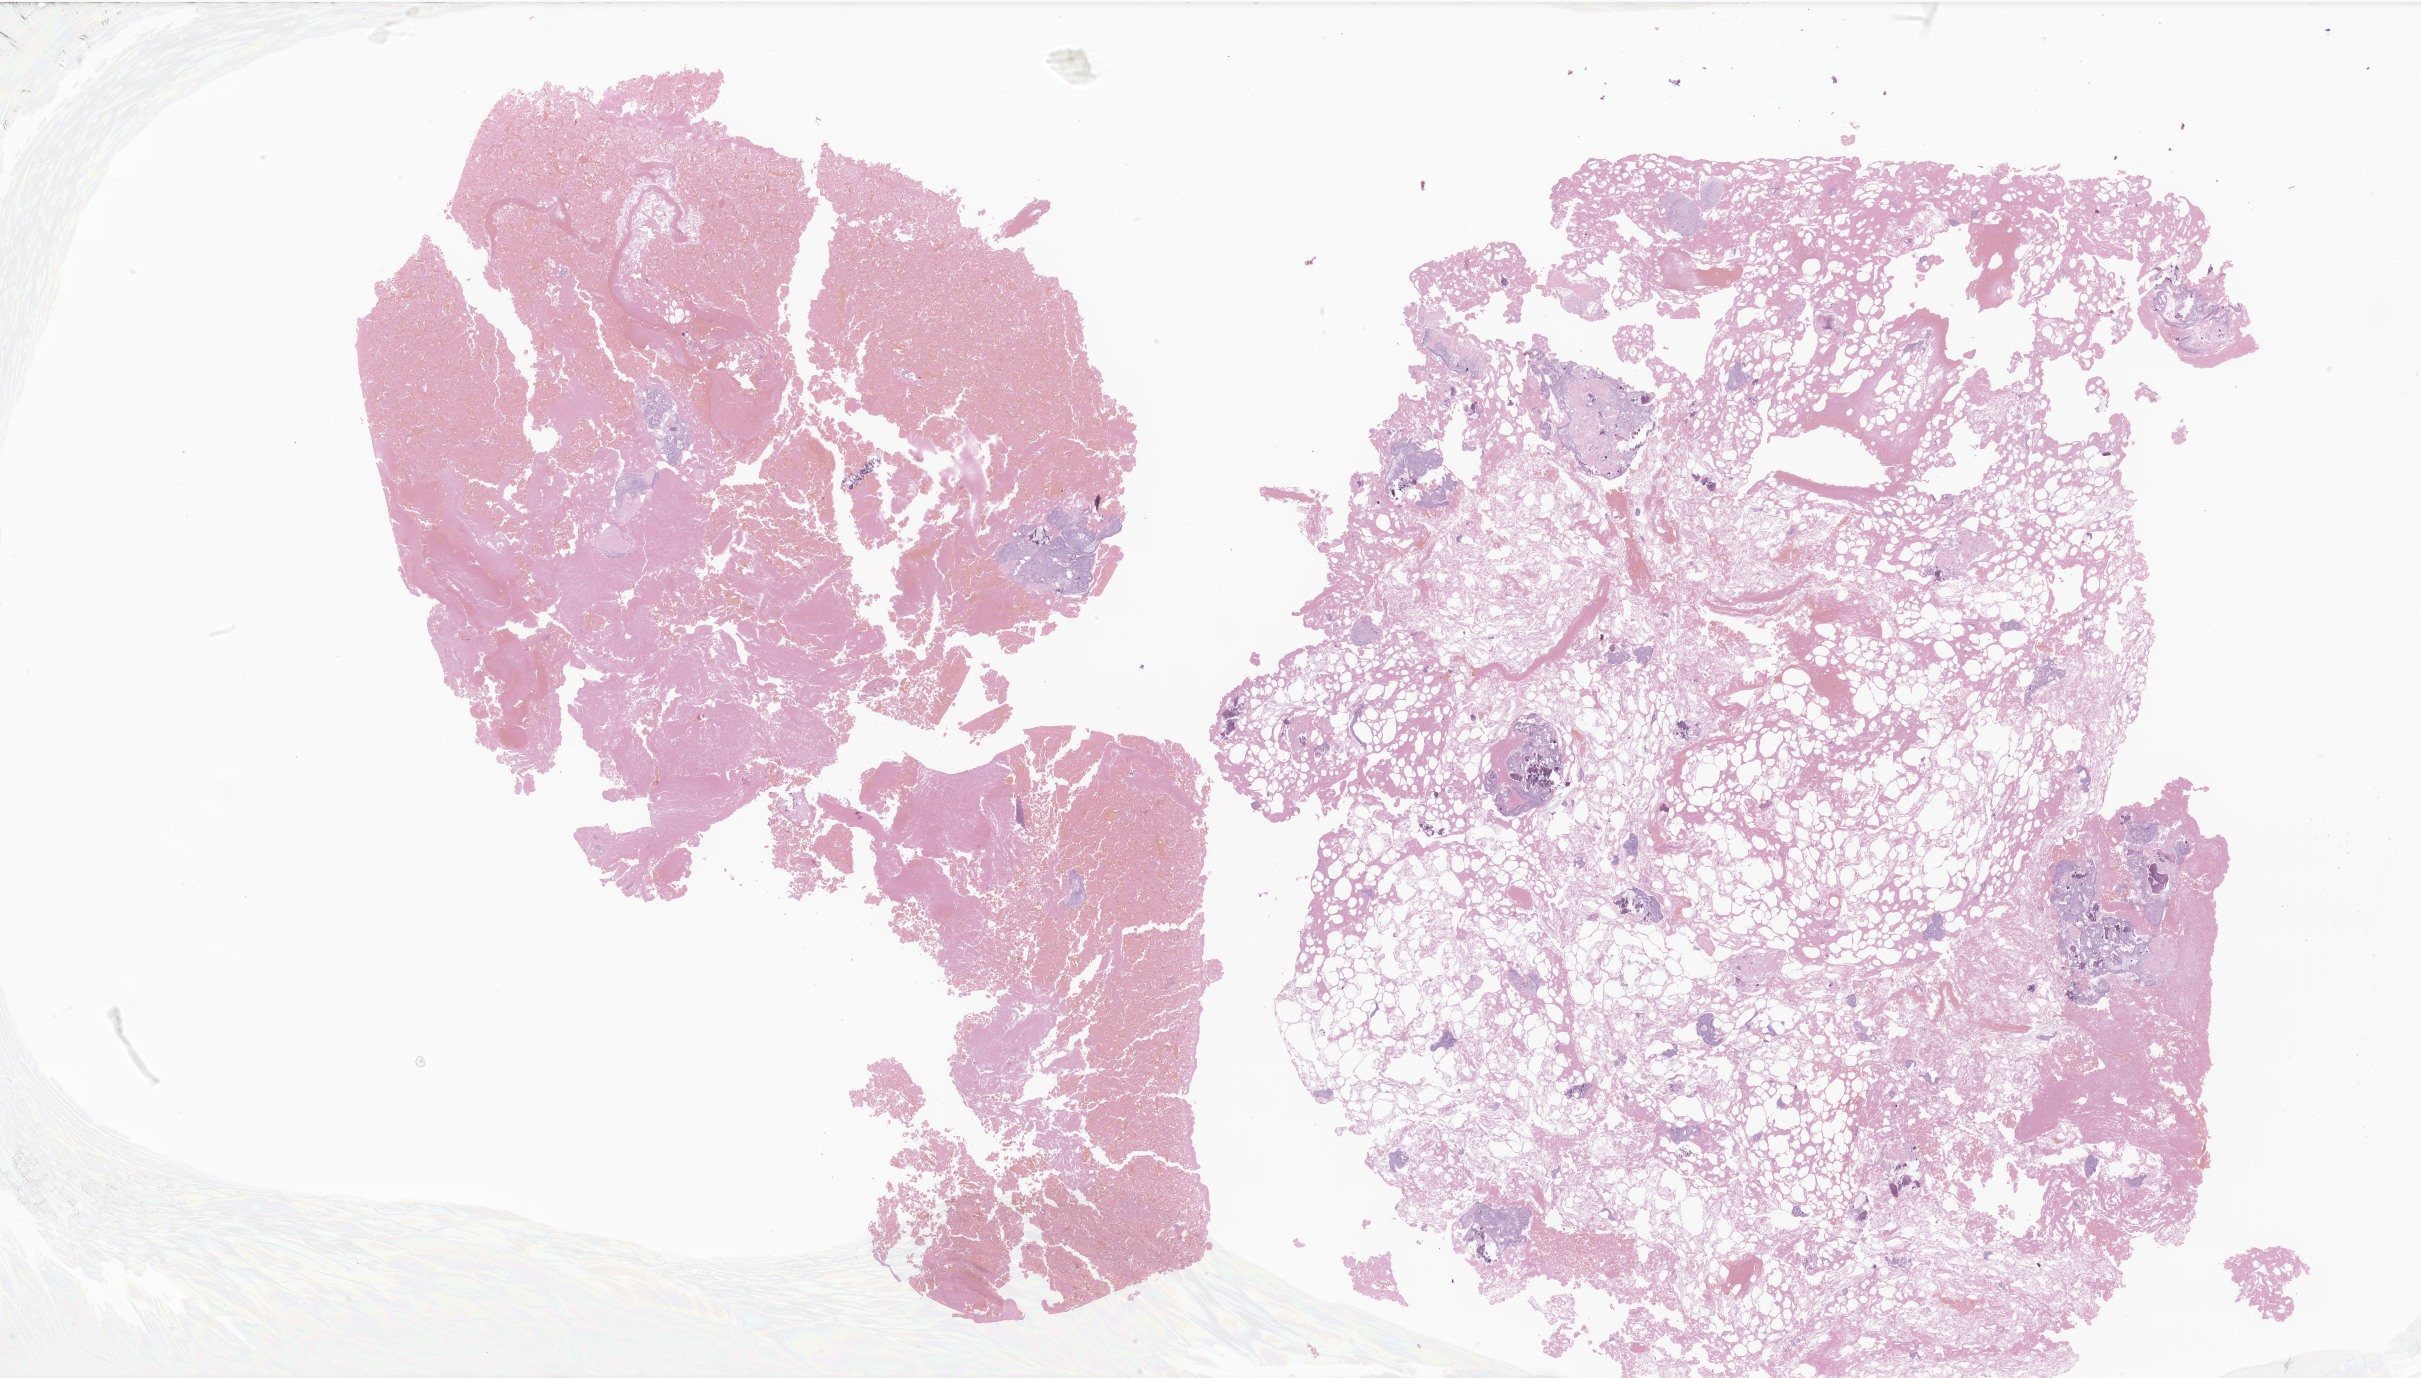
Digitized haematoxylin and eosin-stained section of tumor tissue from the brain — whole scanned area (about 40.8 x 23.2 mm) shown as a low-resolution overview, formalin-fixed paraffin-embedded section. Patient male; age 108 months (9 years).
Recorded diagnosis: Craniopharyngioma, NOS.